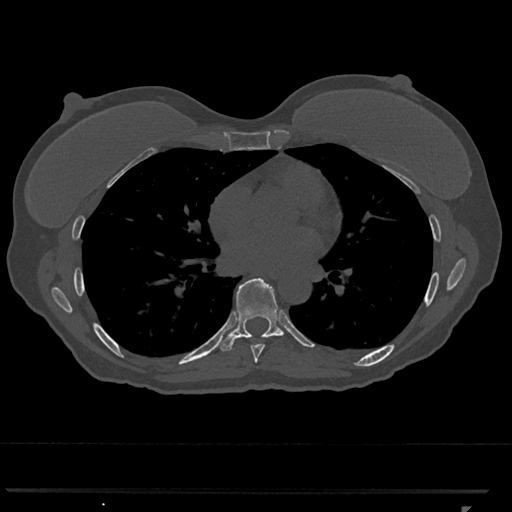
CT including the spine, one axial slice. Position 684 of 793 along the scan axis. Reconstruction kernel Br40s/3. Bone window (W 1800 / L 400 HU). 0.5 mm slice thickness. 512 × 512 image matrix. Patient: female, 62 years. From the clinical record (not read from this slice): primary cancer: renal.
Outlined on this slice (semi-automatically segmented with operator editing):
- T7 vertebra: box from (x=251, y=344) to (x=265, y=363) px
- T8 vertebra: (x=219, y=278)–(x=284, y=351)